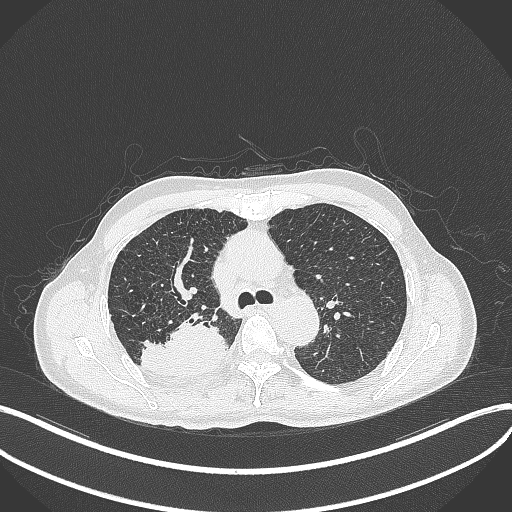
Chest CT, one axial slice. Slice 310 of 428 in the series (ordered by position). Reconstruction kernel B70f. 120 kVp. Lung window (W 1500 / L -600 HU). 1 mm slice thickness. 512 × 512 image matrix. Patient: male, 79 years. From the clinical record (not read from this slice): clinical TNM (as recorded): T3 N0 M0.
Annotated regions visible in this slice (bounding box drawn by a radiologist):
- lung tumour (recorded histology: adenocarcinoma): bounding box [x1, y1, x2, y2] px = [140, 313, 230, 380]